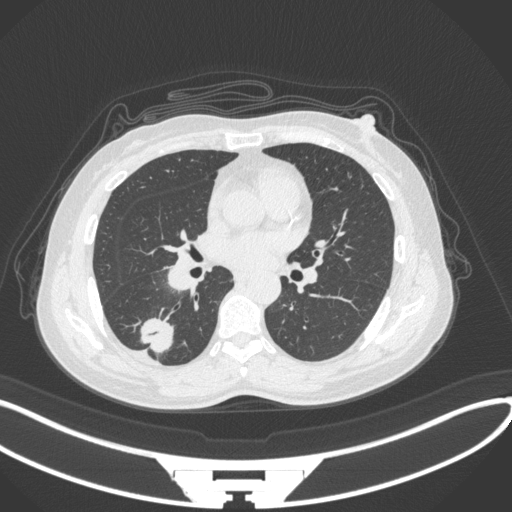
Chest CT, one axial slice. Slice 151 of 352 in the series (ordered by position). Reconstruction kernel B31f. 120 kVp. Lung window (W 1500 / L -600 HU). 1 mm slice thickness. 512 × 512 image matrix, field of view 400 × 400 mm. Patient: female, 55 years. Case-level facts recorded for this patient, not image findings: clinical TNM (as recorded): T1c N1 M0.
Annotated regions visible in this slice (bounding box drawn by a radiologist):
- lung tumour (recorded histology: adenocarcinoma): bounding box <135,314,179,356> (left, top, right, bottom; pixels)